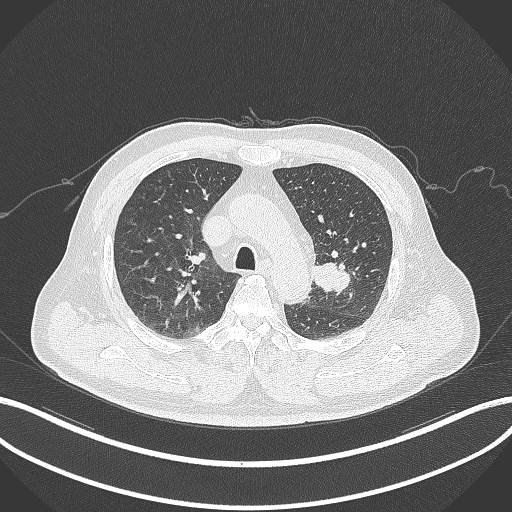
Chest CT, one axial slice; slice 215 of 286 in the series (ordered by position); reconstruction kernel B70f; 120 kVp; lung window (W 1500 / L -600 HU); 1 mm slice thickness; 512 × 512 image matrix, field of view 400 × 400 mm. Patient: male, 67 years. From the clinical record (not read from this slice): clinical TNM (as recorded): T2a N1 M0; histopathological grade: G3.
Structures marked on this image (rectangle marked by the reading radiologist):
- lung tumour (recorded histology: adenocarcinoma): bounding box <308,260,352,293> (left, top, right, bottom; pixels)